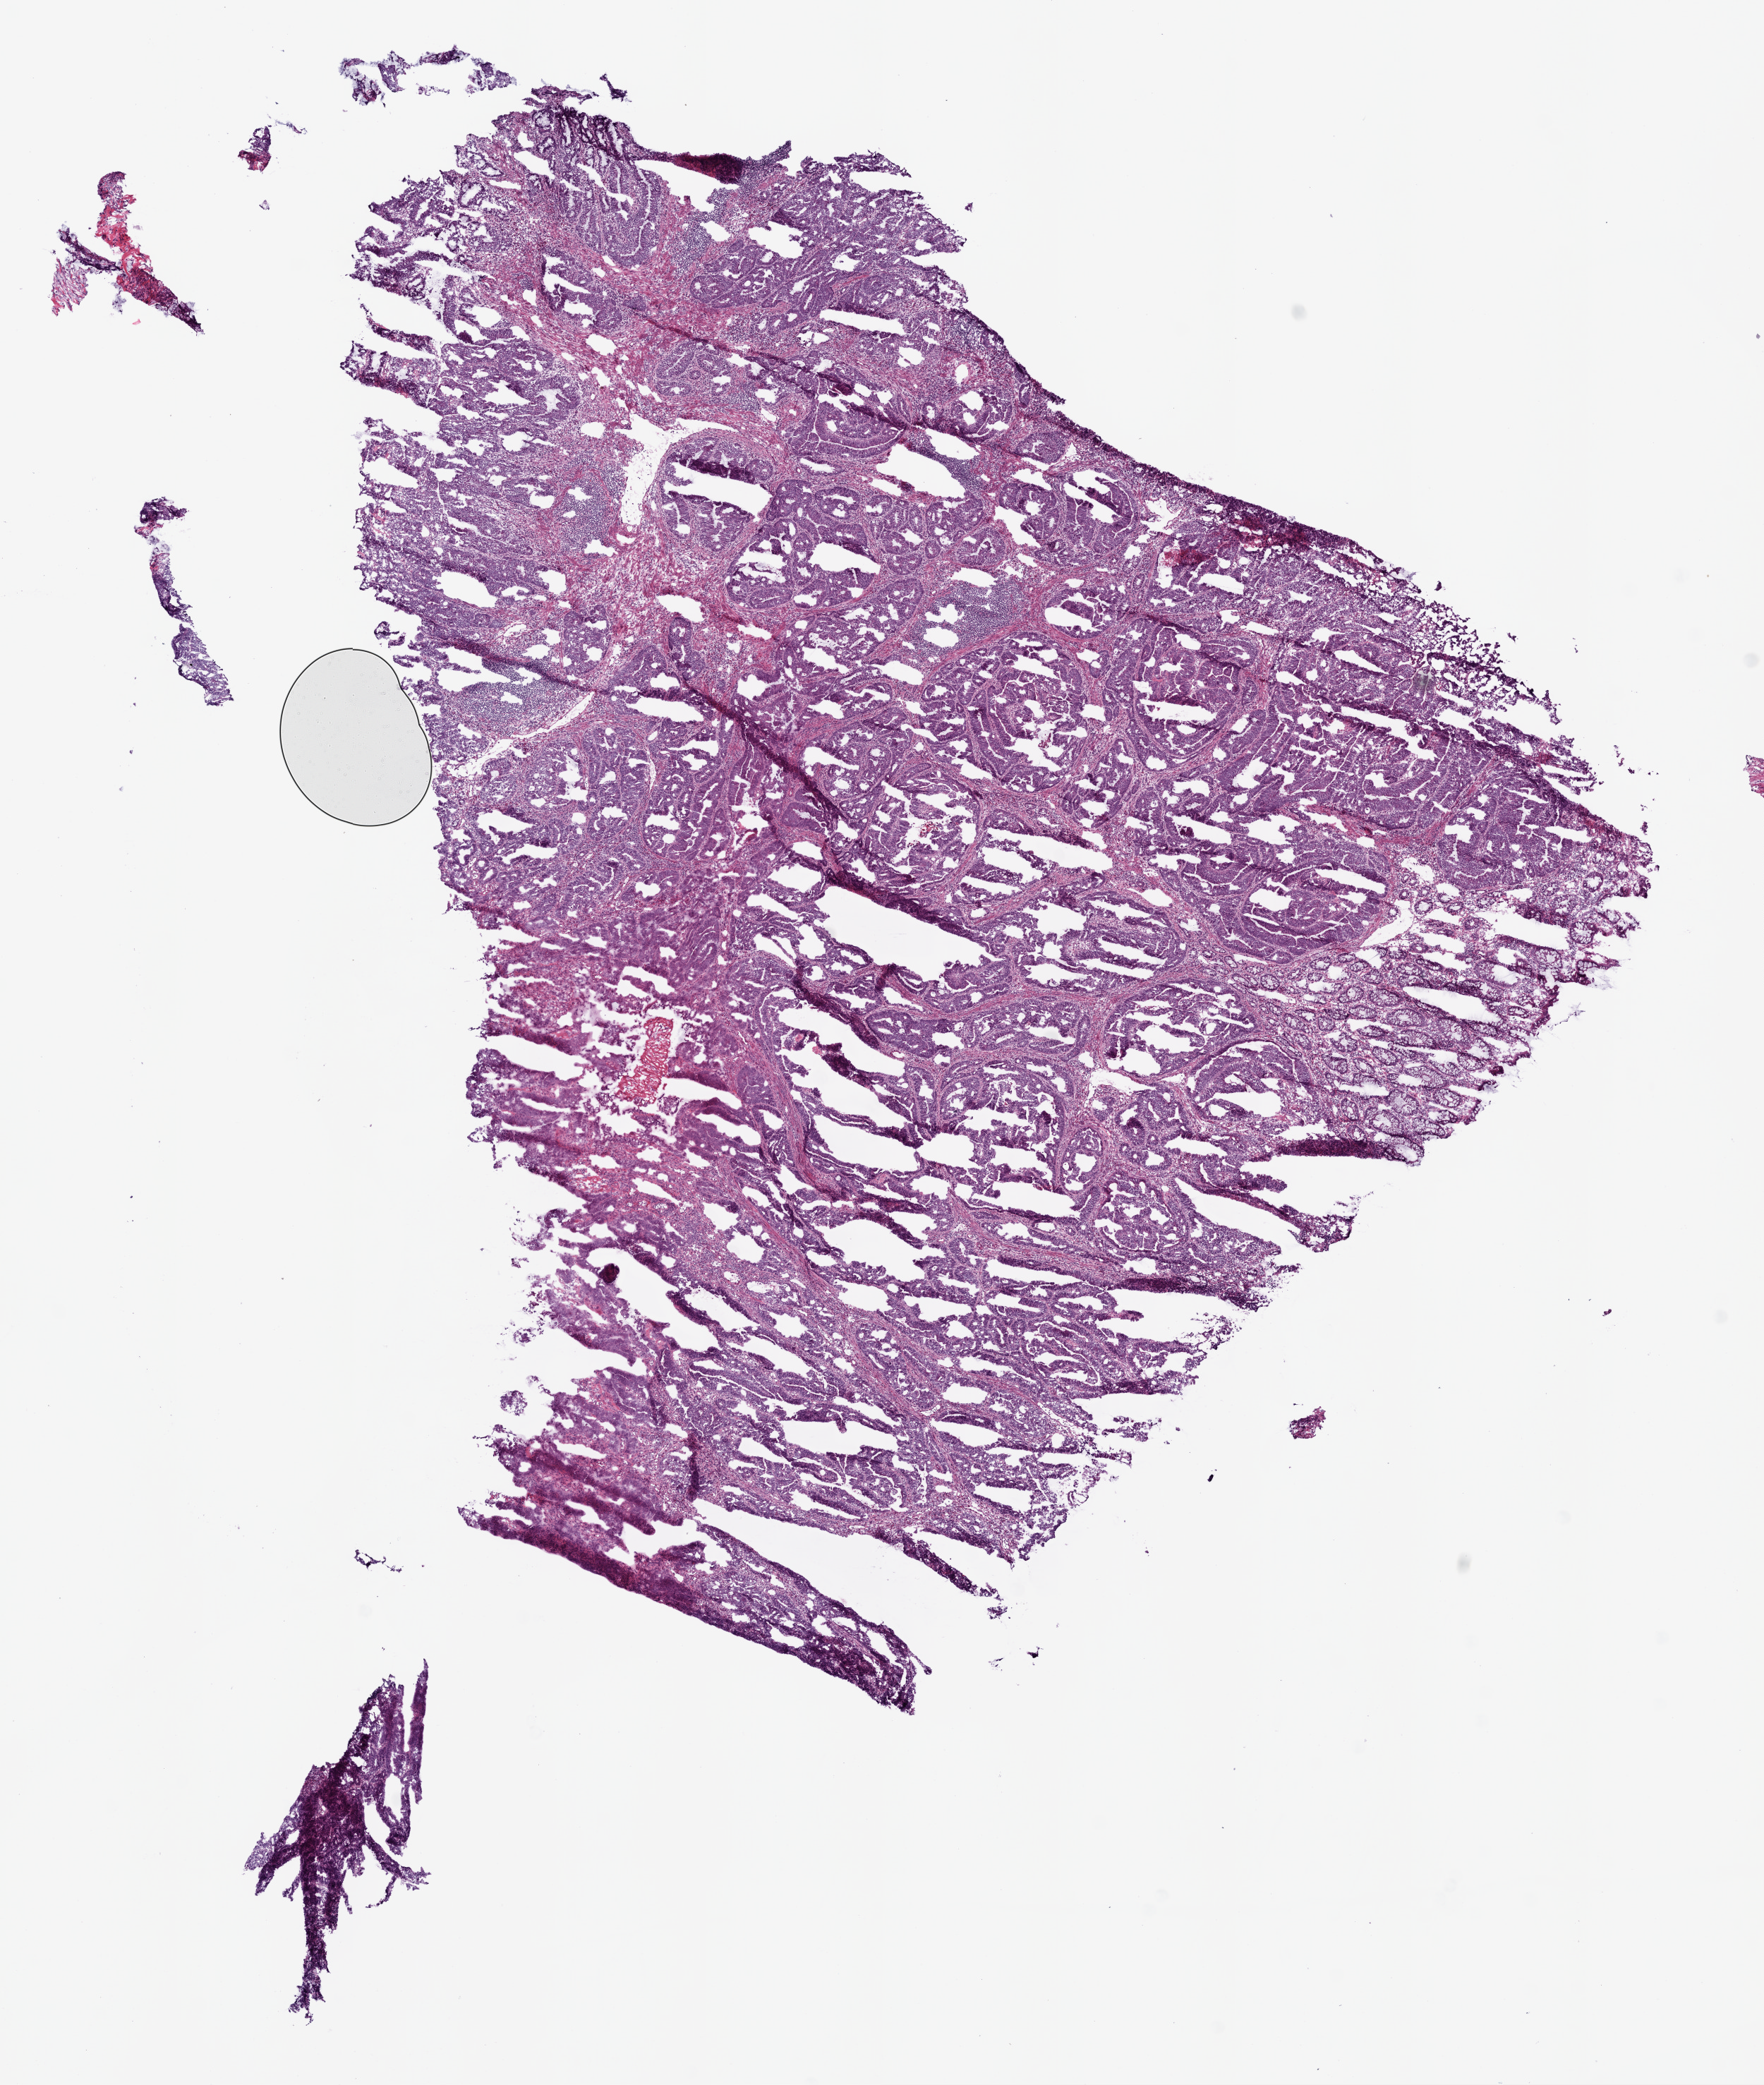
Digitized Hematoxylin and eosin (H&E) stained tissue section (whole slide) — low-resolution overview of the scanned area, about 10.0 x 11.9 mm; frozen section from the bottom of the tissue portion; colon, primary tumour sample. Female, age 53 years at initial diagnosis. Slide review estimates, as recorded: tumour cells 75%, tumour nuclei 80%, normal cells 2%, stromal cells 18%, necrosis 5%.
Diagnosis: Adenocarcinoma, NOS. Lymph nodes positive (case pathology): 0 of 41 examined. AJCC pathologic stage: II (5th edition). TNM: T3 N0 M0.